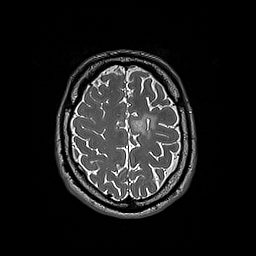
Brain MRI from a brain-tumour surgery series, one axial slice. Slice 55 of 192 in the series (ordered by position). 1 mm slice thickness. 256 × 256 image matrix. Case-level facts recorded for this patient, not image findings: histopathology: Oligodendroglioma; WHO grade: 3; IDH mutation: yes; tumour location: Left Frontal.
Outlined on this slice (manually delineated by an expert):
- tumour: bounding box (x1, y1, x2, y2) in pixels: (131, 114, 157, 136)